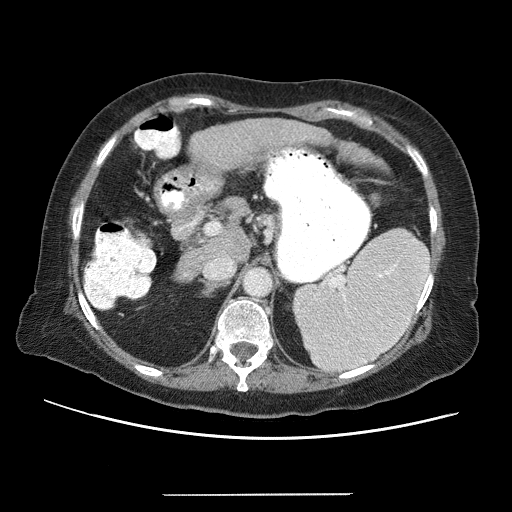
Contrast-enhanced abdominal CT (liver protocol), one axial slice. Slice 32 of 65 in the series (ordered by position). Reconstruction kernel STANDARD. 120 kVp. Soft-tissue window (W 400 / L 40 HU). 512 × 512 image matrix, field of view 380 × 380 mm. Case-level facts recorded for this patient, not image findings: diagnosis: hepatocellular carcinoma (patient treated with transarterial chemoembolisation; whether this scan precedes or follows treatment is not stated here); TNM stage (as recorded): Stage-IIIB; Child-Pugh class: A; tumour differentiation: moderately differentiated; tumour nodularity: uninodular.
Structures marked on this image (semi-automatic segmentation, software-assisted and operator-edited):
- liver parenchyma outside the tumour (the mass and vessels are separate outlines, so this box may not span the whole liver): bounding box [x1, y1, x2, y2] px = [173, 118, 388, 280]
- liver vessels: [211, 134, 296, 257]